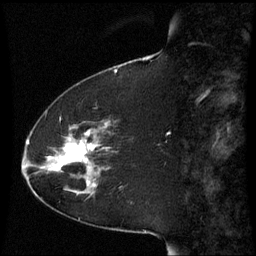
Breast MRI (dynamic contrast-enhanced), one sagittal slice. Dynamic contrast-enhanced series, image 2 of 3 at this slice position (ordered by acquisition). 1.5 T. TE 4.2 ms, TR 8.9 ms. 2.3 mm slice thickness. 256 × 256 image matrix, field of view 210 × 210 mm. Patient: female, 51 years. Case-level facts recorded for this patient, not image findings: setting: breast cancer imaged before/during neoadjuvant chemotherapy; receptor status: HR-positive, HER2-negative.
Structures marked on this image (semi-automatic segmentation, software-assisted and operator-edited):
- analysis volume of interest (the breast-tissue region the enhancement analysis was run in; not a lesion): bounding box [x1, y1, x2, y2] px = [50, 120, 112, 187]
- tumour enhancement mask (voxels above the 70 % enhancement threshold inside the analysis volume of interest): [53, 141, 96, 187]